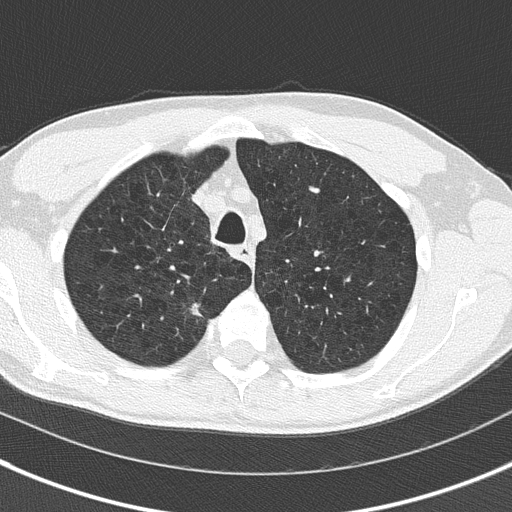
Low-dose screening chest CT, axial slice; baseline screening round; lung window (W 1500 / L -600 HU); slice 37 of 175 in the series. Male, age 56 years at enrolment.
Expert reader's lesion annotation, bounding box <179,294,221,338> (left, top, right, bottom; pixels). The screening reader recorded 3 non-calcified nodules or masses ≥4 mm on this exam (right upper lobe, right upper lobe, left lower lobe); which of them this box marks is not recorded. Official screen result: positive, change unspecified: nodule(s) >= 4 mm or enlarging nodule(s), mass(es), or other non-specific abnormalities suspicious for lung cancer. Later outcome: lung cancer diagnosed 228 days after this screen — non-small cell carcinoma, right upper lobe, stage IIIA (AJCC 6th edition), 21 mm at pathology.